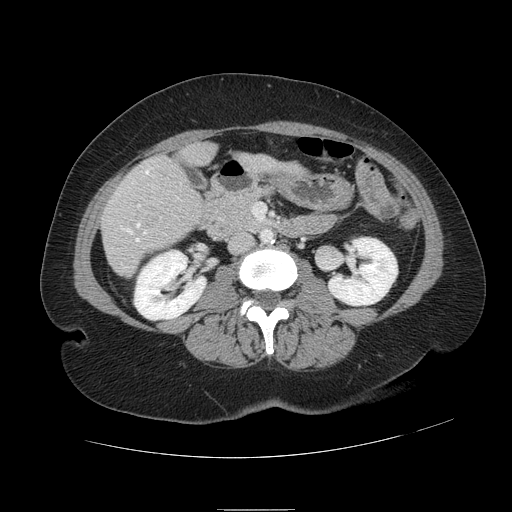
Contrast-enhanced abdominal CT, one axial slice. Position 28 of 121 along the scan axis. Soft-tissue window (W 400 / L 40 HU). 2.5 mm slice thickness. 512 × 512 image matrix, field of view 400 × 400 mm. Female patient, age 52 years. Case-level facts recorded for this patient, not image findings: diagnosis: colorectal cancer liver metastases, imaged before liver resection; multiple liver metastases: yes; largest metastasis: 6.3 cm; disease in both lobes: no.
Annotated regions visible in this slice (expert manual segmentation):
- hepatic veins: bounding box (x1, y1, x2, y2) in pixels: (124, 171, 149, 242)
- liver: (102, 145, 270, 276)
- planned liver remnant (the part of the liver to remain after resection): (184, 145, 270, 169)
- portal vein (with intrahepatic branches): (138, 205, 140, 208)